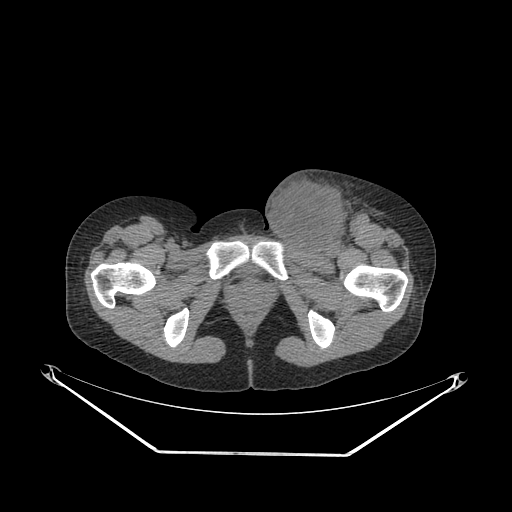
CT of an extremity soft-tissue mass (from a PET/CT study), one axial slice; slice 62 of 267 in the series (ordered by position); soft-tissue window (W 400 / L 40 HU); 3.75 mm slice thickness; 512 × 512 image matrix, field of view 500 × 500 mm. Female patient. From the clinical record (not read from this slice): histological type: leiomyosarcoma; grade: high; site of the primary tumour: groin.
Annotated regions visible in this slice (expert contour drawn on MRI and transferred to this co-registered scan by the dataset authors):
- gross tumour volume including surrounding oedema: box from (x=260, y=171) to (x=380, y=254) px
- gross tumour volume (mass): (x=262, y=178)–(x=346, y=252)